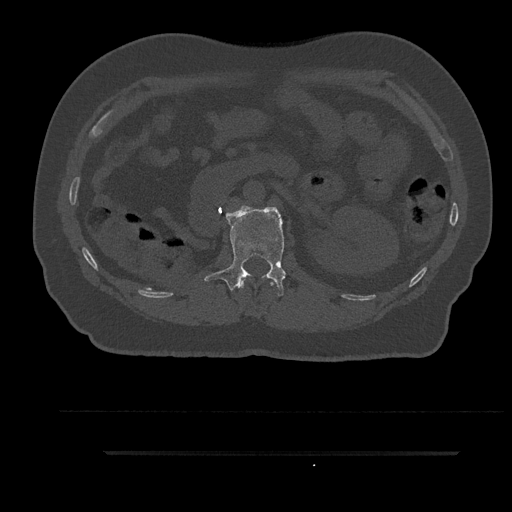
CT including the spine, one axial slice. Slice 181 of 797 in the series (ordered by position). Reconstruction kernel Br40s/3. Bone window (W 1800 / L 400 HU). 512 × 512 image matrix, field of view 432 × 432 mm. Patient: male, 63 years. Case-level facts recorded for this patient, not image findings: primary cancer: renal; vertebrae with lytic lesions (as recorded): T8.
Outlined on this slice (semi-automatic segmentation, software-assisted and operator-edited):
- L1 vertebra: bounding box (x1, y1, x2, y2) in pixels: (204, 206, 286, 296)
- T12 vertebra: (240, 279, 274, 289)